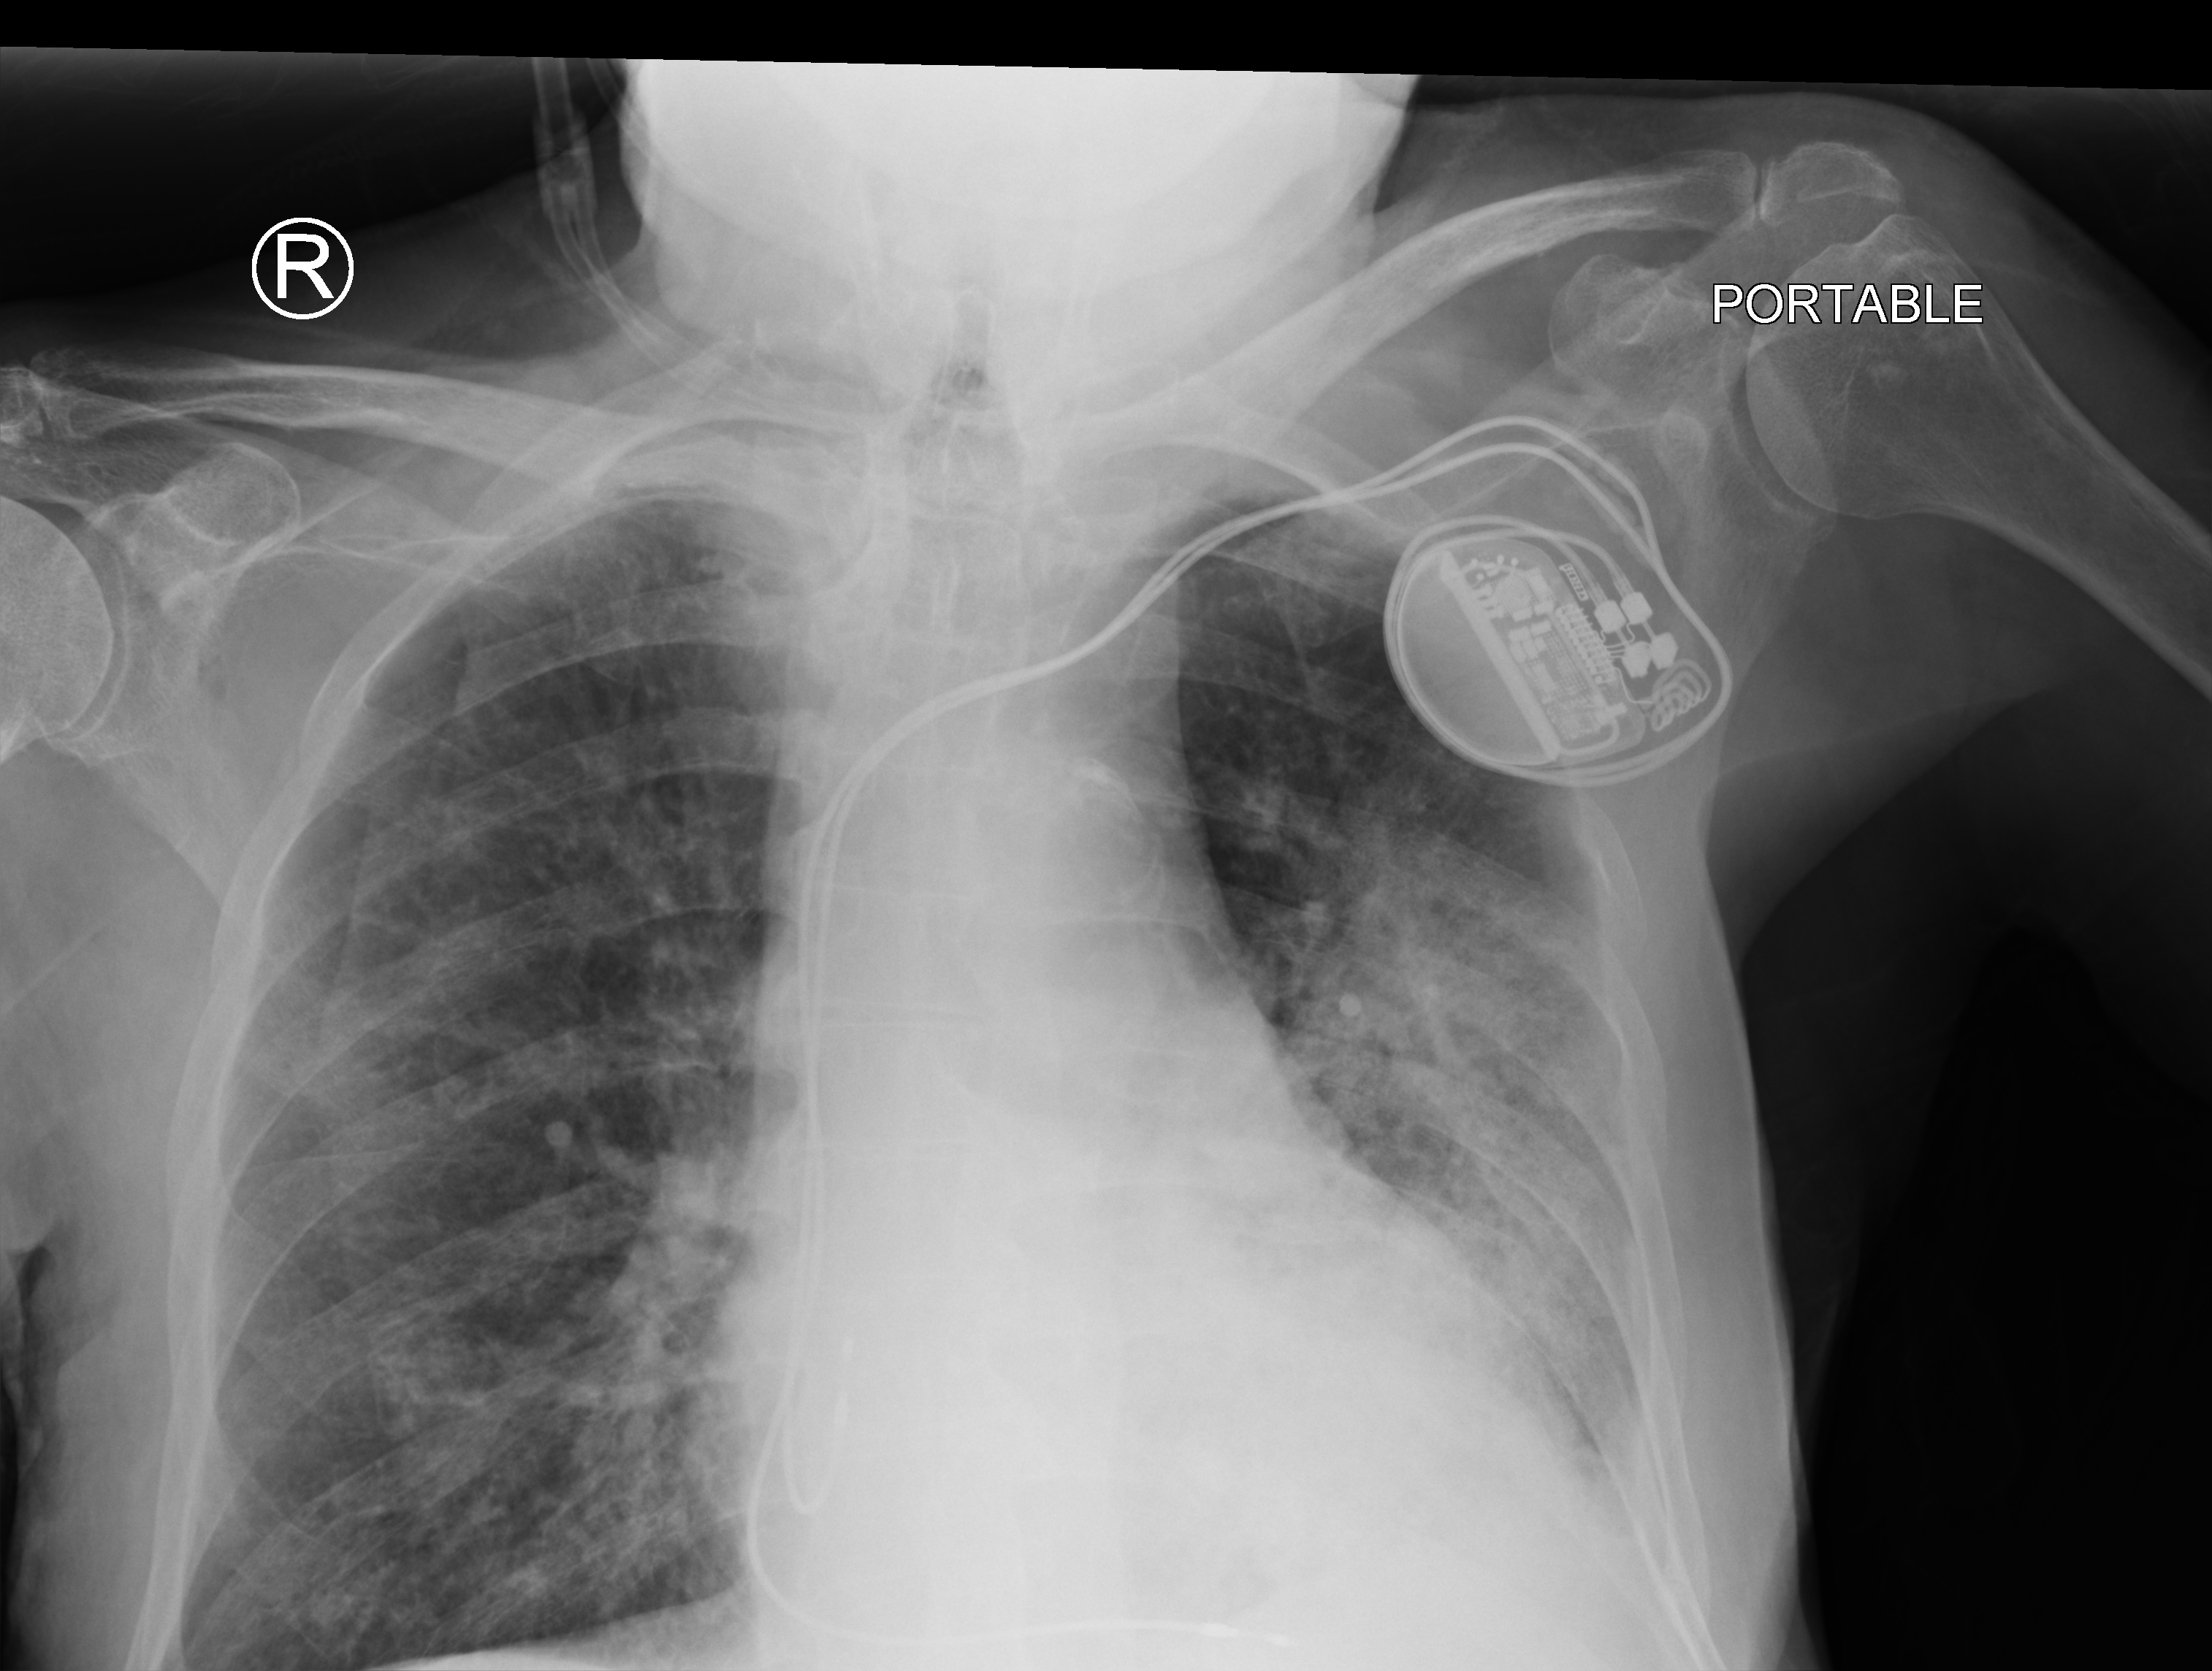
Portable chest radiograph; anteroposterior (AP) projection. Male patient hospitalised with COVID-19, age 75–90 years.
Hospital-stay facts (about this admission, not read from this image; timing relative to this image not recorded): admitted to intensive care during this hospital stay: no; length of hospital stay: 5 days; mechanically ventilated during this hospital stay: no.